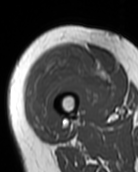
MRI of an extremity soft-tissue mass, one axial slice; slice 30 of 99 in the series (ordered by position); MR volume resampled by the dataset authors to the PET/CT grid (not the native acquisition matrix); 138 × 172 image matrix, field of view 135 × 168 mm. Female patient. Case-level facts recorded for this patient, not image findings: histological type: pleiomorphic undifferentiated sarcoma; grade: high; site of the primary tumour: right quadricep.
Annotated regions visible in this slice (expert contour drawn on MRI and transferred to this co-registered scan by the dataset authors):
- gross tumour volume including surrounding oedema: box from (x=28, y=50) to (x=106, y=128) px
- gross tumour volume (mass): (x=39, y=52)–(x=104, y=78)